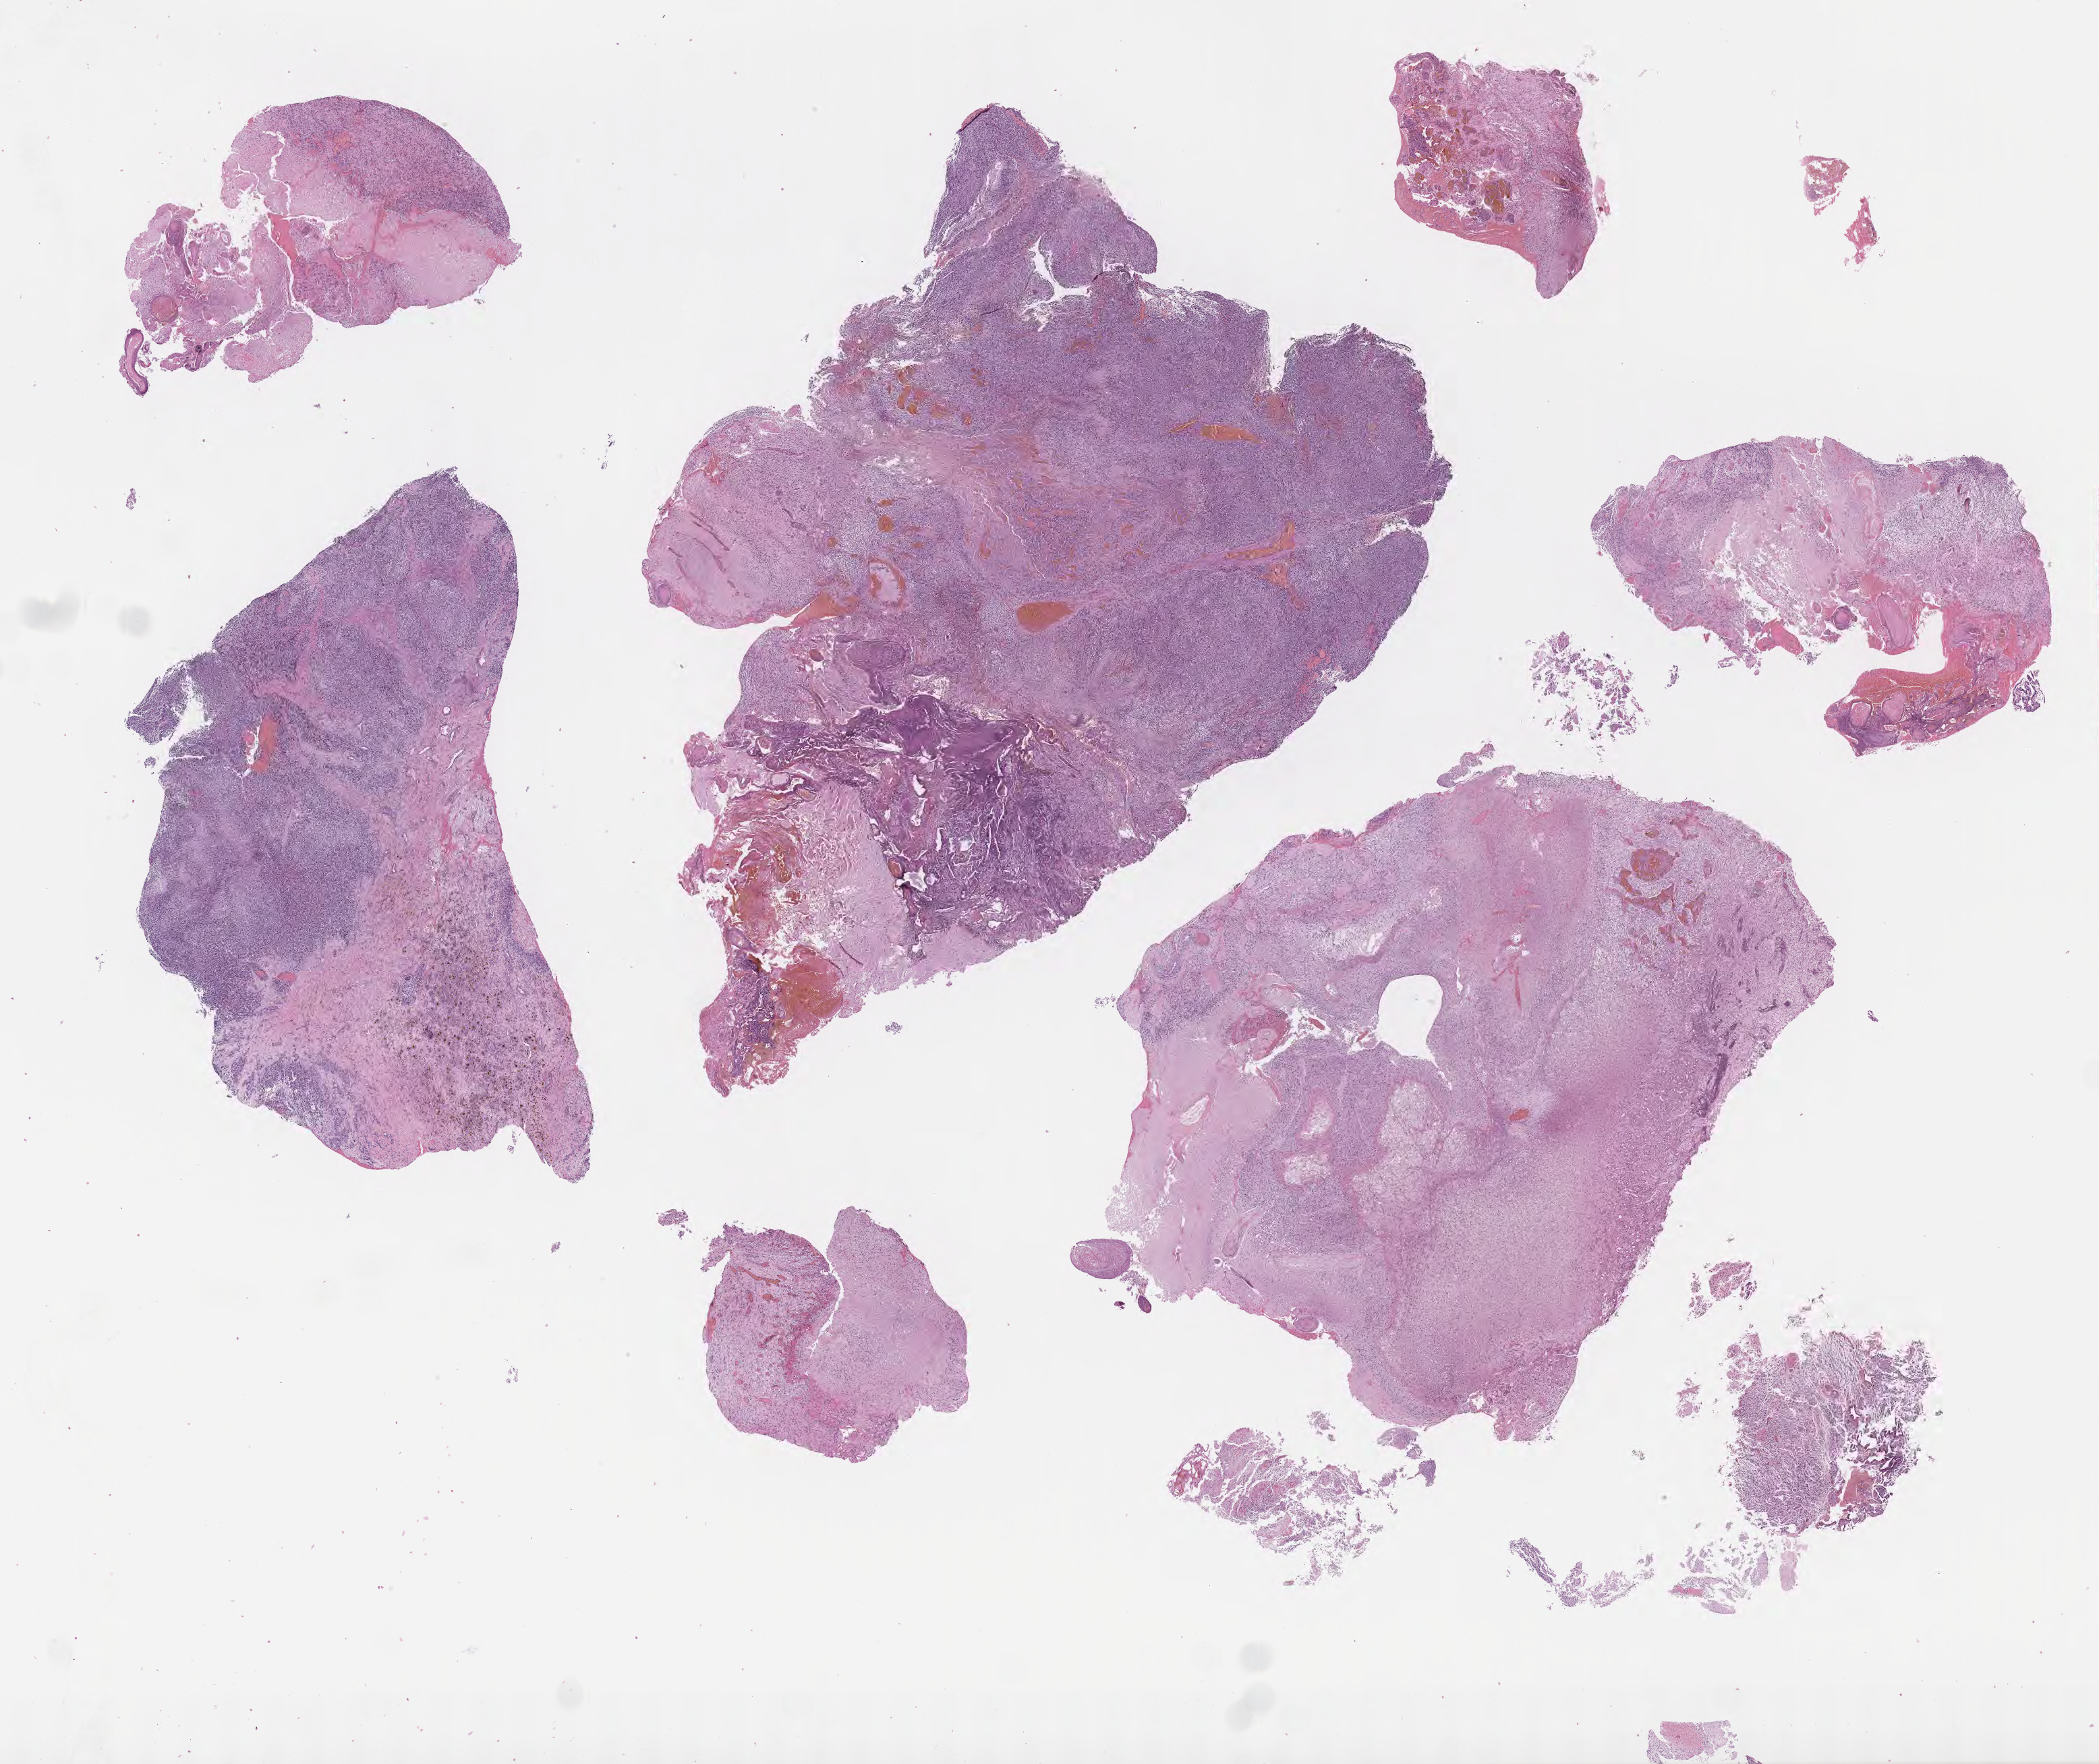
Haematoxylin and eosin whole-slide image — a low-resolution overview of the entire scanned area, about 25.2 x 21.1 mm; formalin-fixed, paraffin-embedded (FFPE) tissue; primary tumor; anatomic site: brain. Male patient; age at initial diagnosis 66 years. Slide review estimates, as recorded: tumor cells 52%, tumor nuclei 71%, stromal cells 17%, necrosis 10%, normal cells 21%. Inflammatory infiltration, as recorded: lymphocyte infiltration 2%, monocyte infiltration 1%, neutrophil infiltration 1%.
Section: top of the tissue portion. Diagnosis: Glioblastoma, NOS.